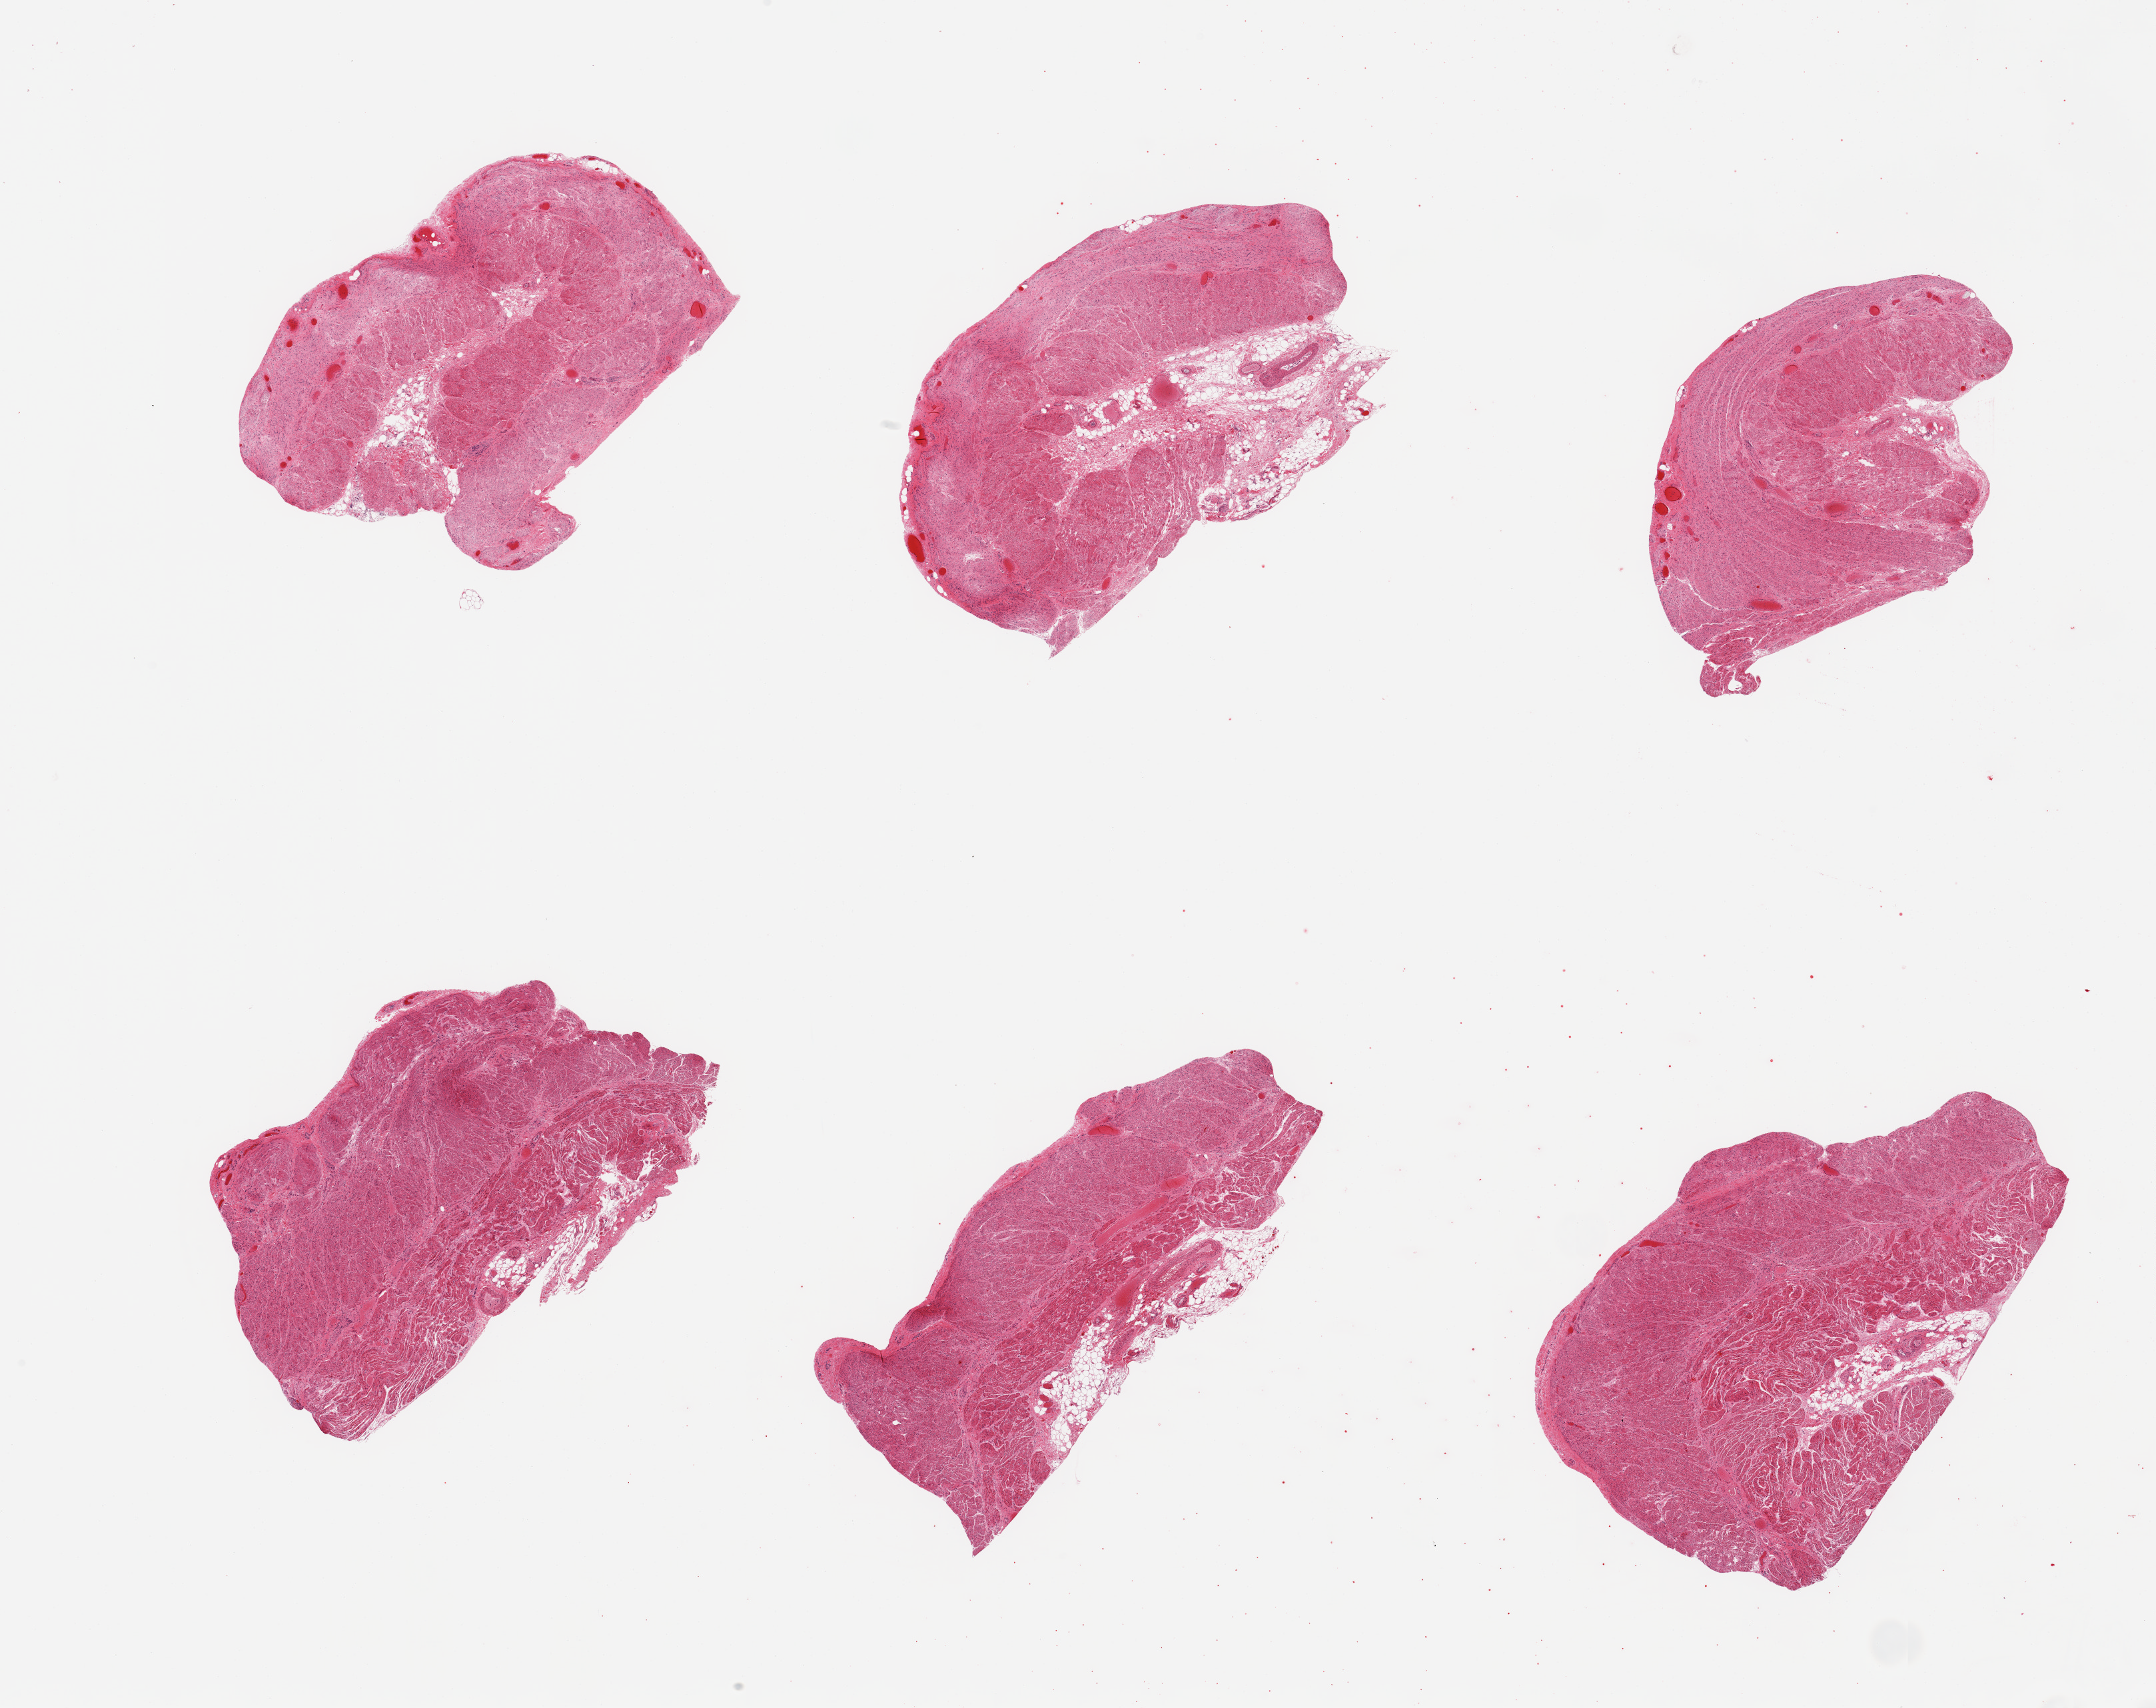
H&E whole-slide image — shown as a low-resolution overview of the whole scanned area (about 25.6 x 20.3 mm, acquisition: 20x scan). PAXgene-fixed paraffin-embedded (PFPE) section. Section of gastroesophageal junction (target tissue). Donor tissue sample. Donor: male.
Reviewer comment on this tissue sample: 6 pieces; target muscularis propria; congestion; up to 2mm attached fat and fibrovascular tissue, 10% overall content.